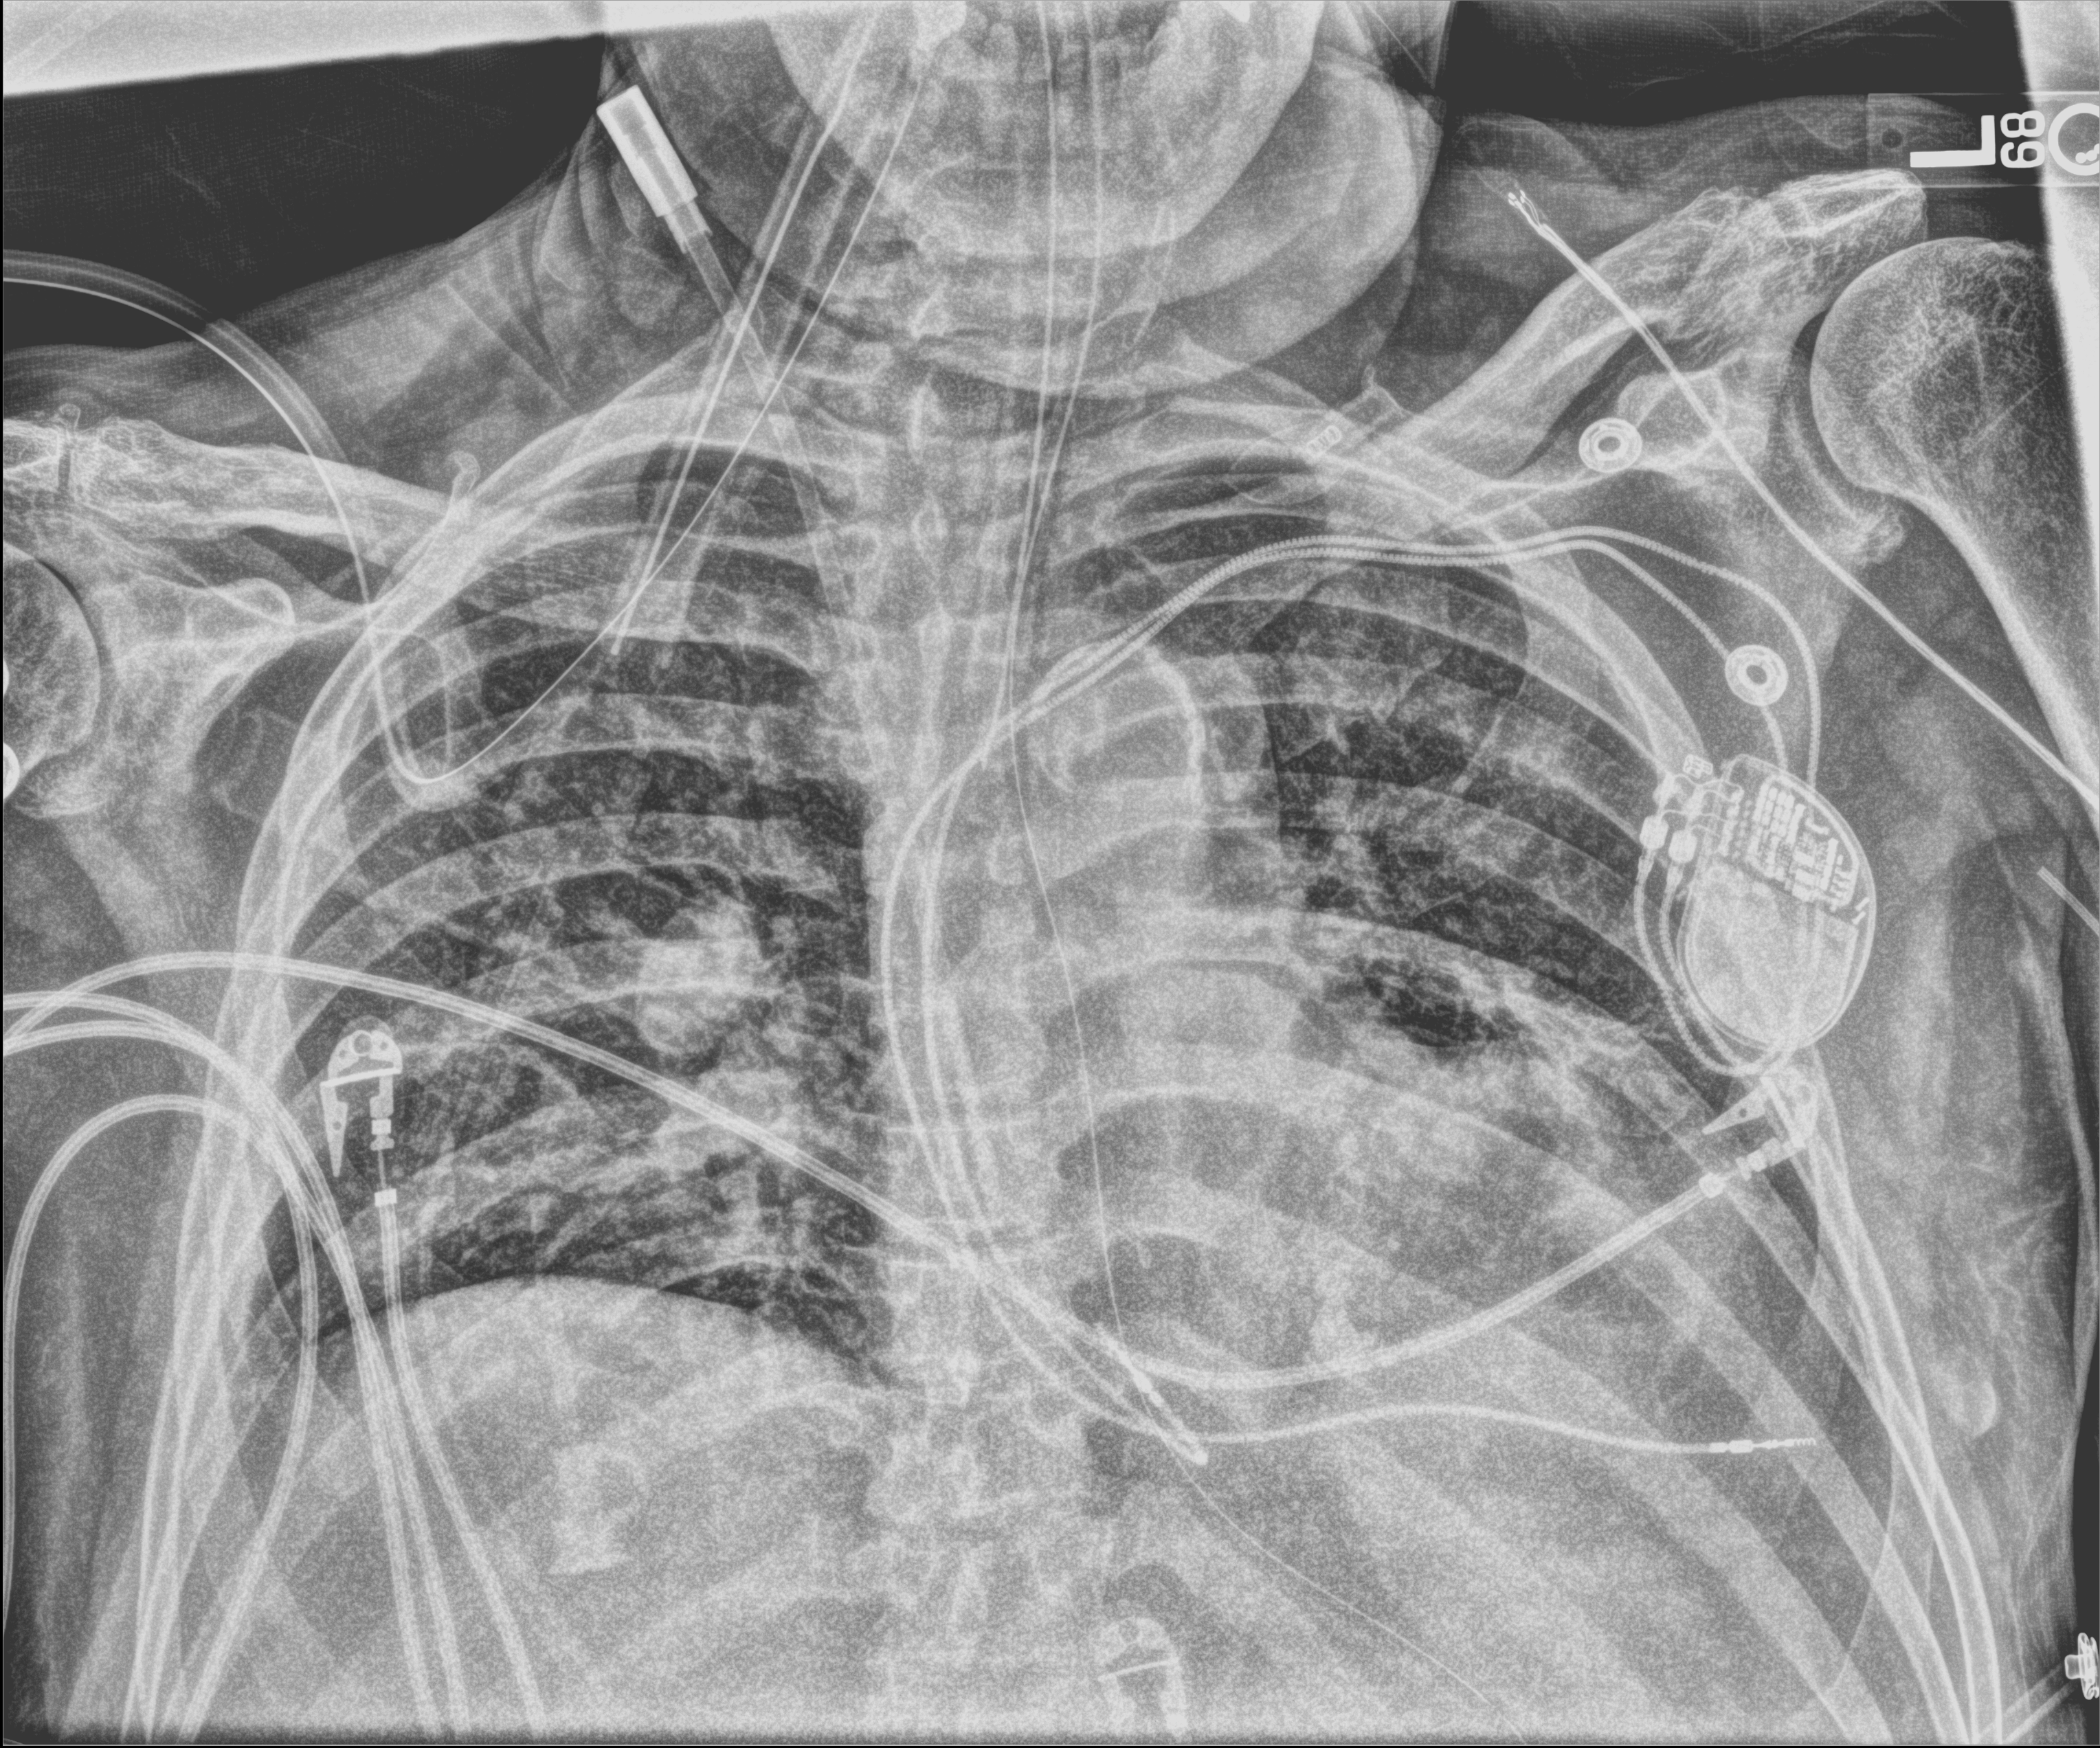
Portable chest radiograph; anteroposterior (AP) projection. Patient hospitalised with COVID-19; male, aged 60–74 years.
From the hospital-stay record, not from the radiograph (when in the stay this image was taken is not recorded):
- admitted to intensive care during this hospital stay: yes